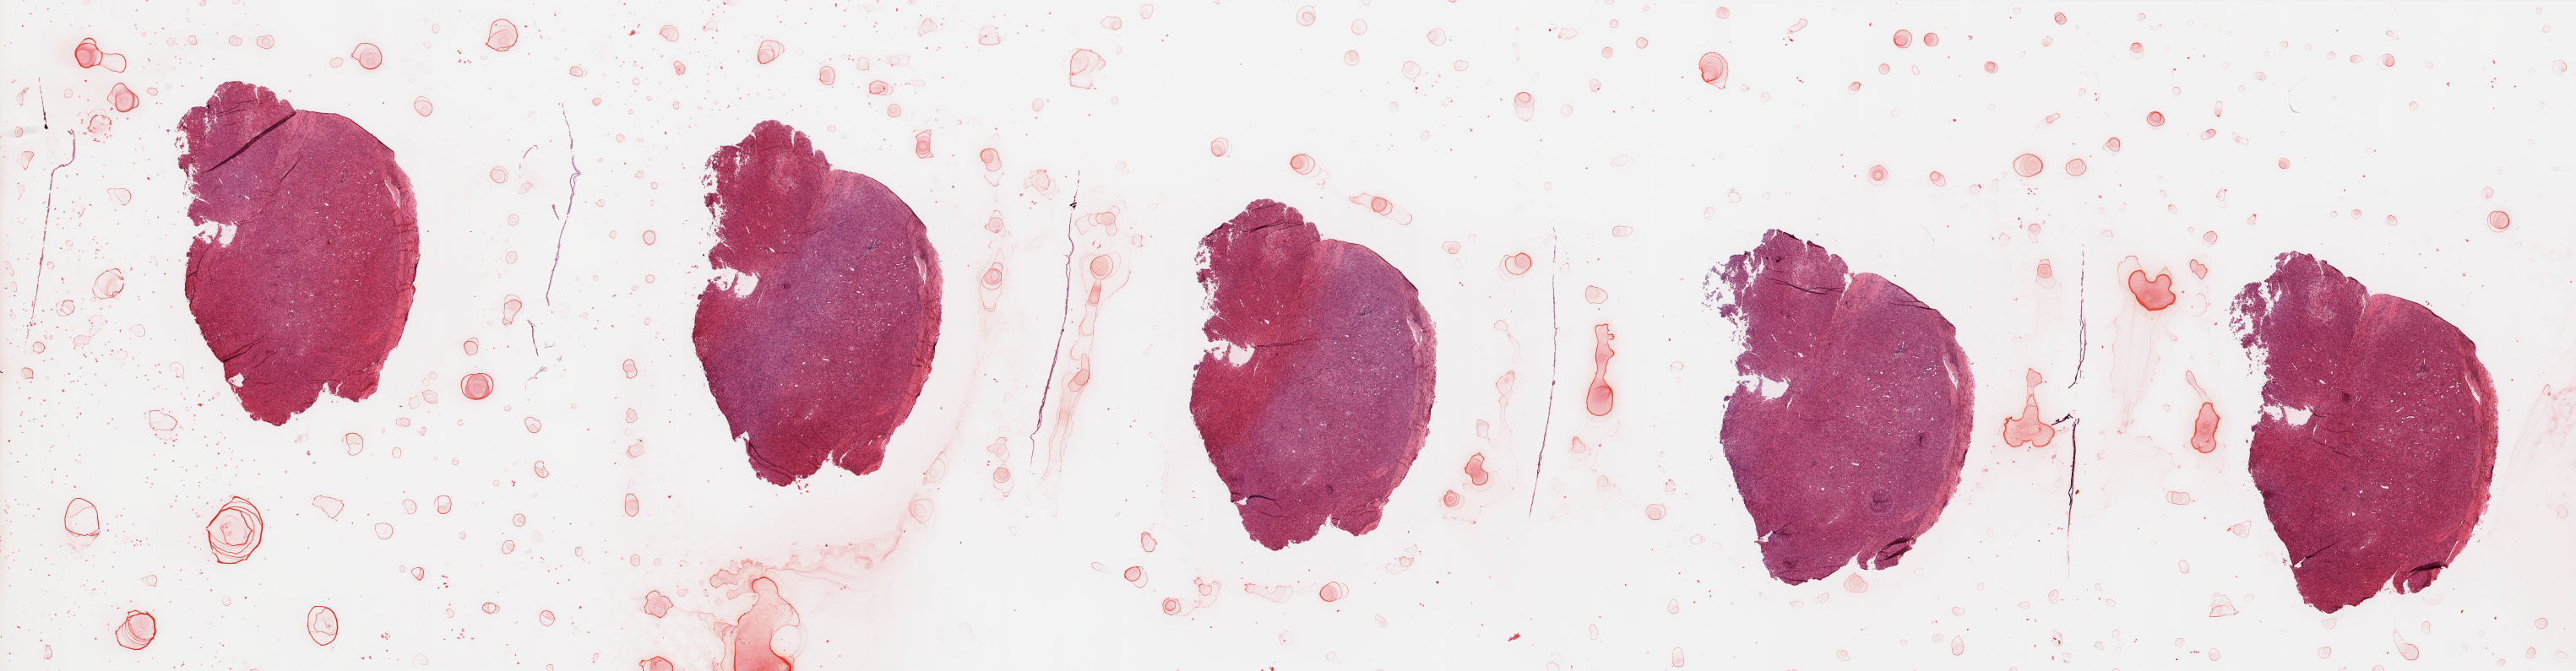
Whole-slide histology image, H&E-stained, low-resolution overview of the scanned area, about 48.2 x 12.6 mm; tumour tissue sample. Patient: female, age 75 years.
• primary tumour site (as recorded): lower extremity
• patient diagnosis (cohort enrolment): sarcoma (site not recorded at cohort level)